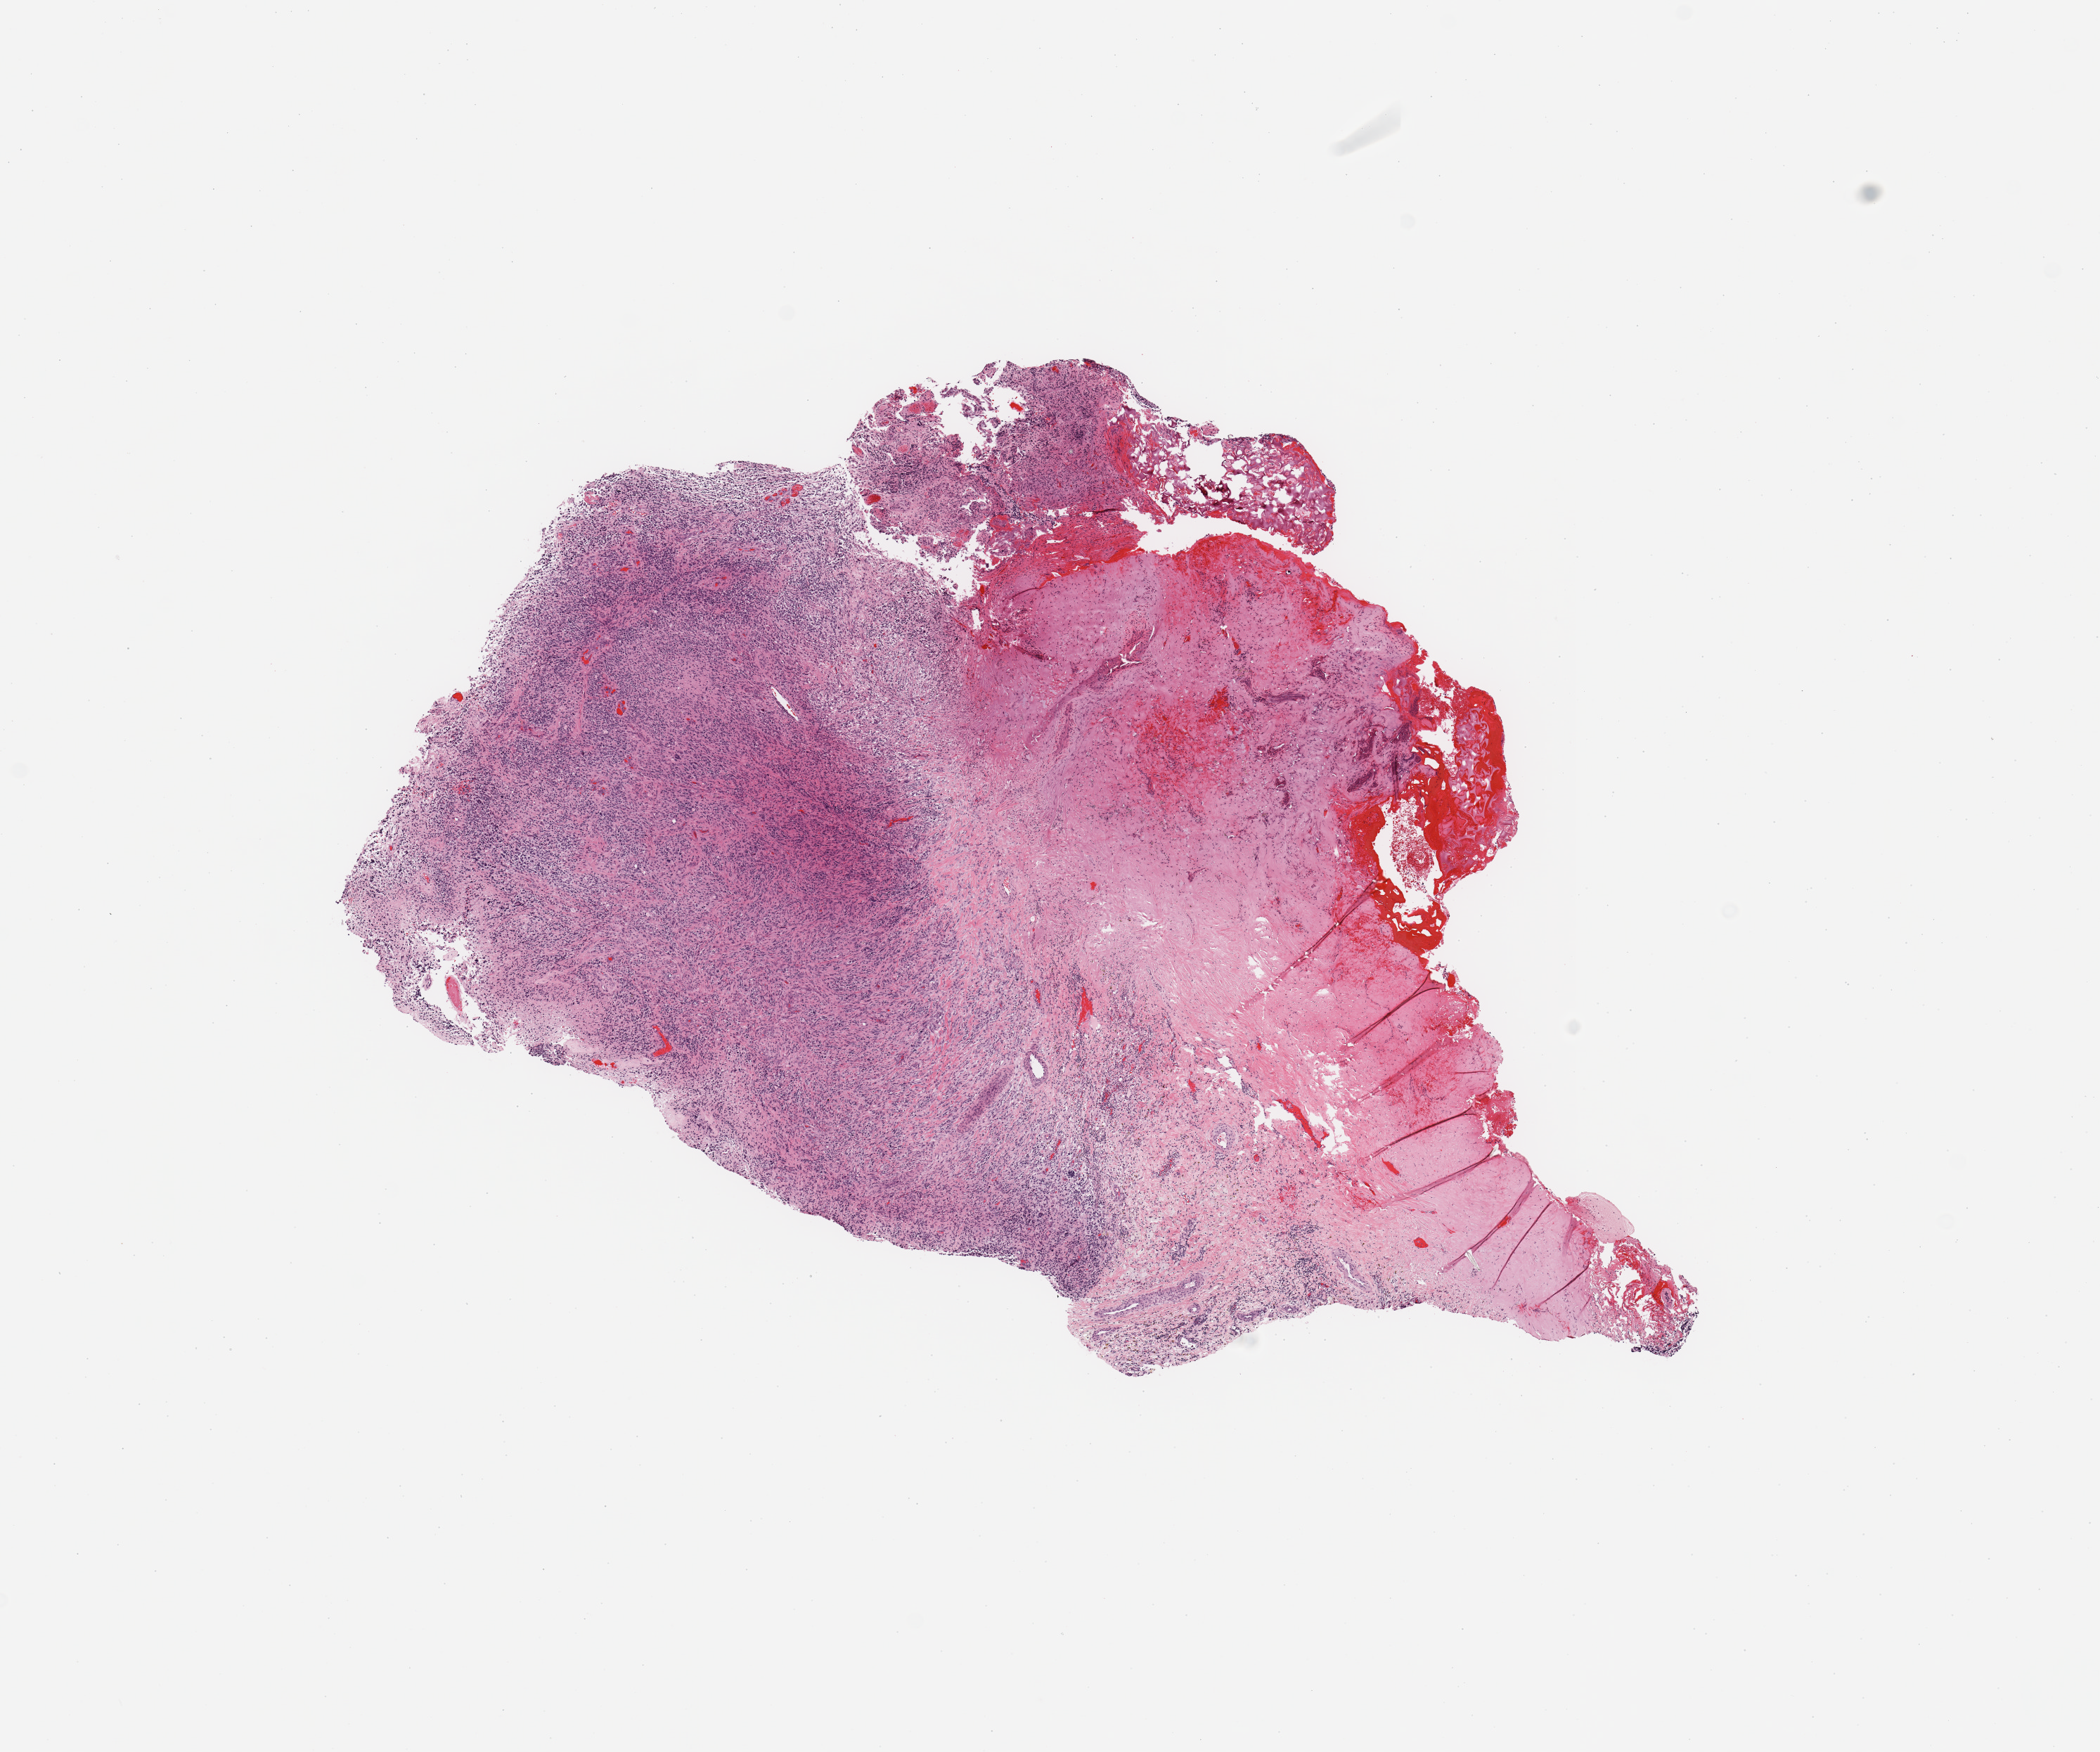
H&E-stained whole-slide image — low-resolution overview of the scanned area, about 11.8 x 9.9 mm, tumour tissue sample, brain. 58-year-old female patient.
* primary tumour site (as recorded): temporal lobe
* histologic diagnosis: Glioblastoma